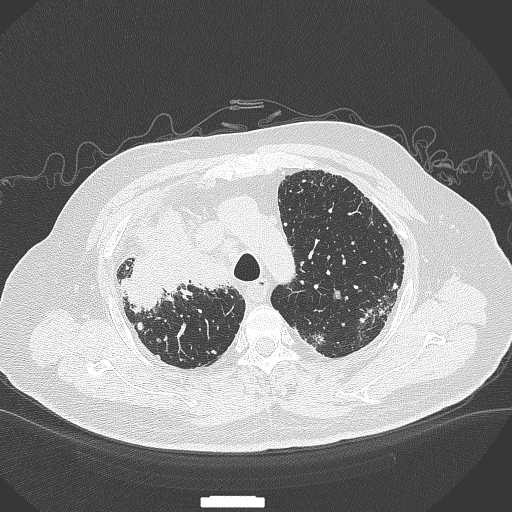
Chest CT, one axial slice. Position 279 of 384 along the scan axis. 120 kVp. Lung window (W 1500 / L -600 HU). 1 mm slice thickness. 512 × 512 image matrix, field of view 400 × 400 mm. Patient: male, 69 years. Case-level facts recorded for this patient, not image findings: clinical TNM (as recorded): T4 N3 M1.
Outlined on this slice (rectangle marked by the reading radiologist):
- lung tumour (recorded histology: adenocarcinoma): bounding box <126,207,227,310> (left, top, right, bottom; pixels)